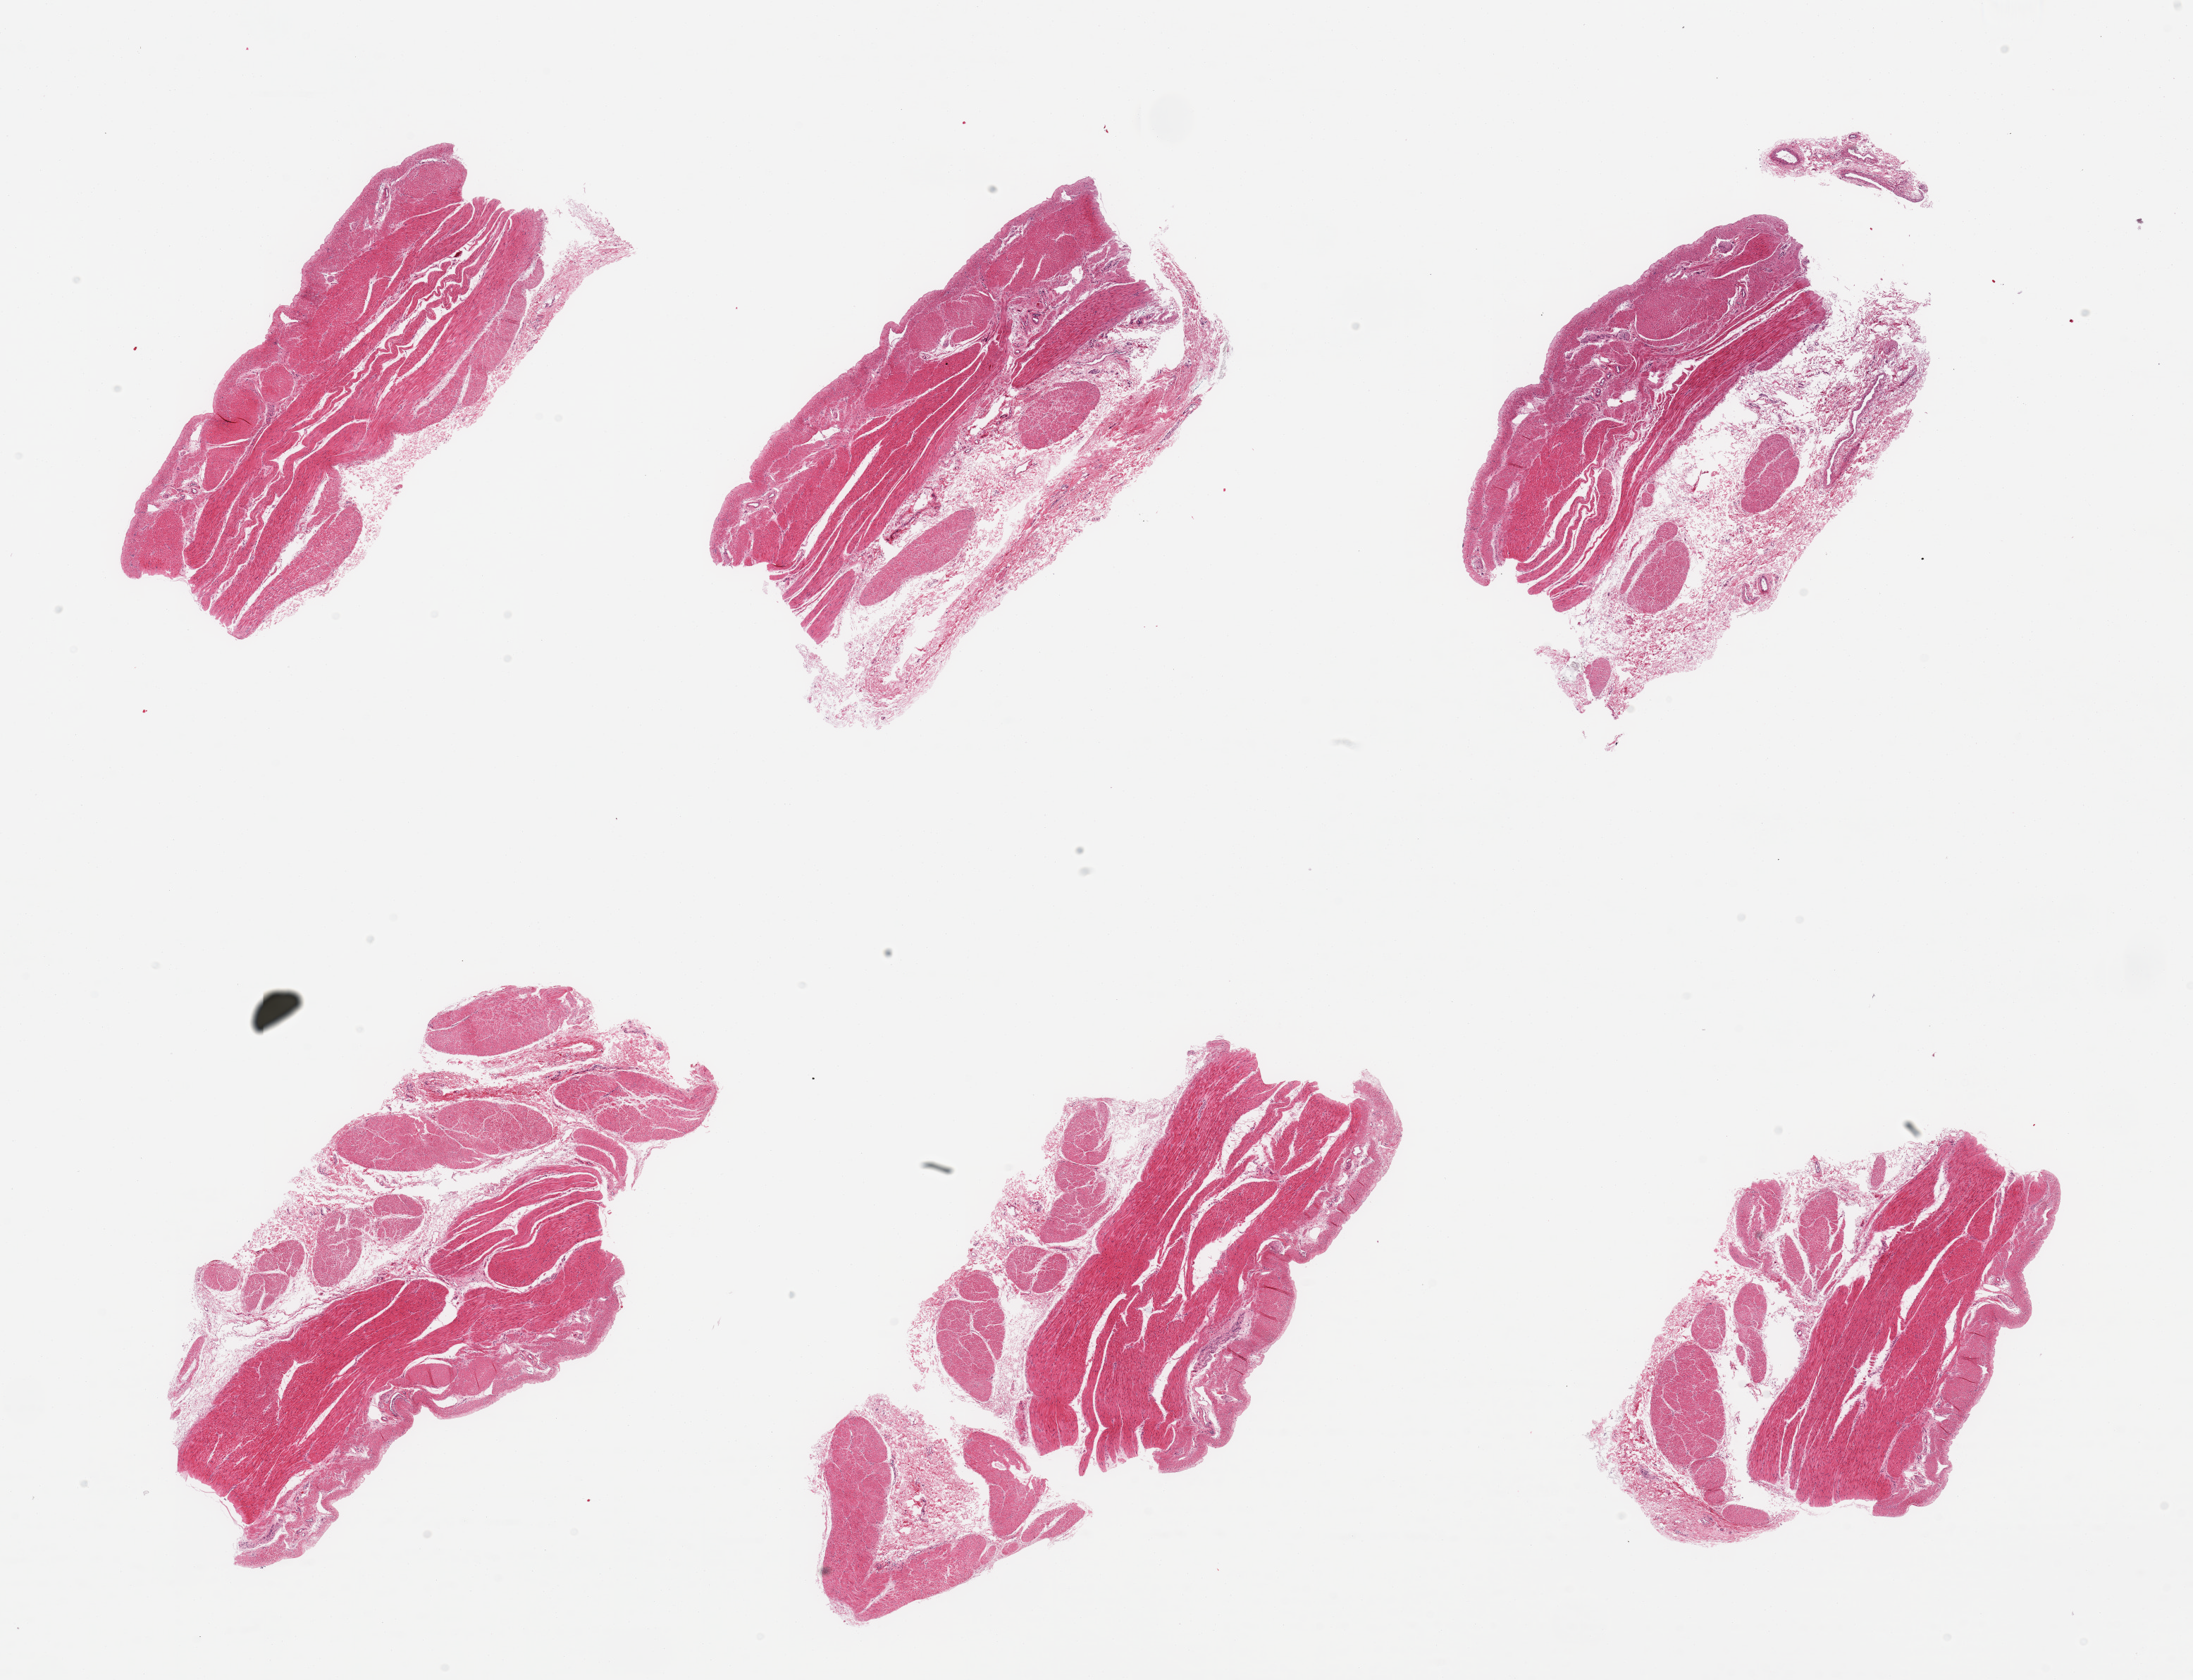
Whole-slide image, H&E stain — shown as a low-resolution overview of the whole scanned area (about 24.6 x 18.9 mm, slide scanned at 20x). Female donor.
* specimen: PAXgene-fixed paraffin-embedded (PFPE) section; section of stomach (target tissue); tissue donor sample